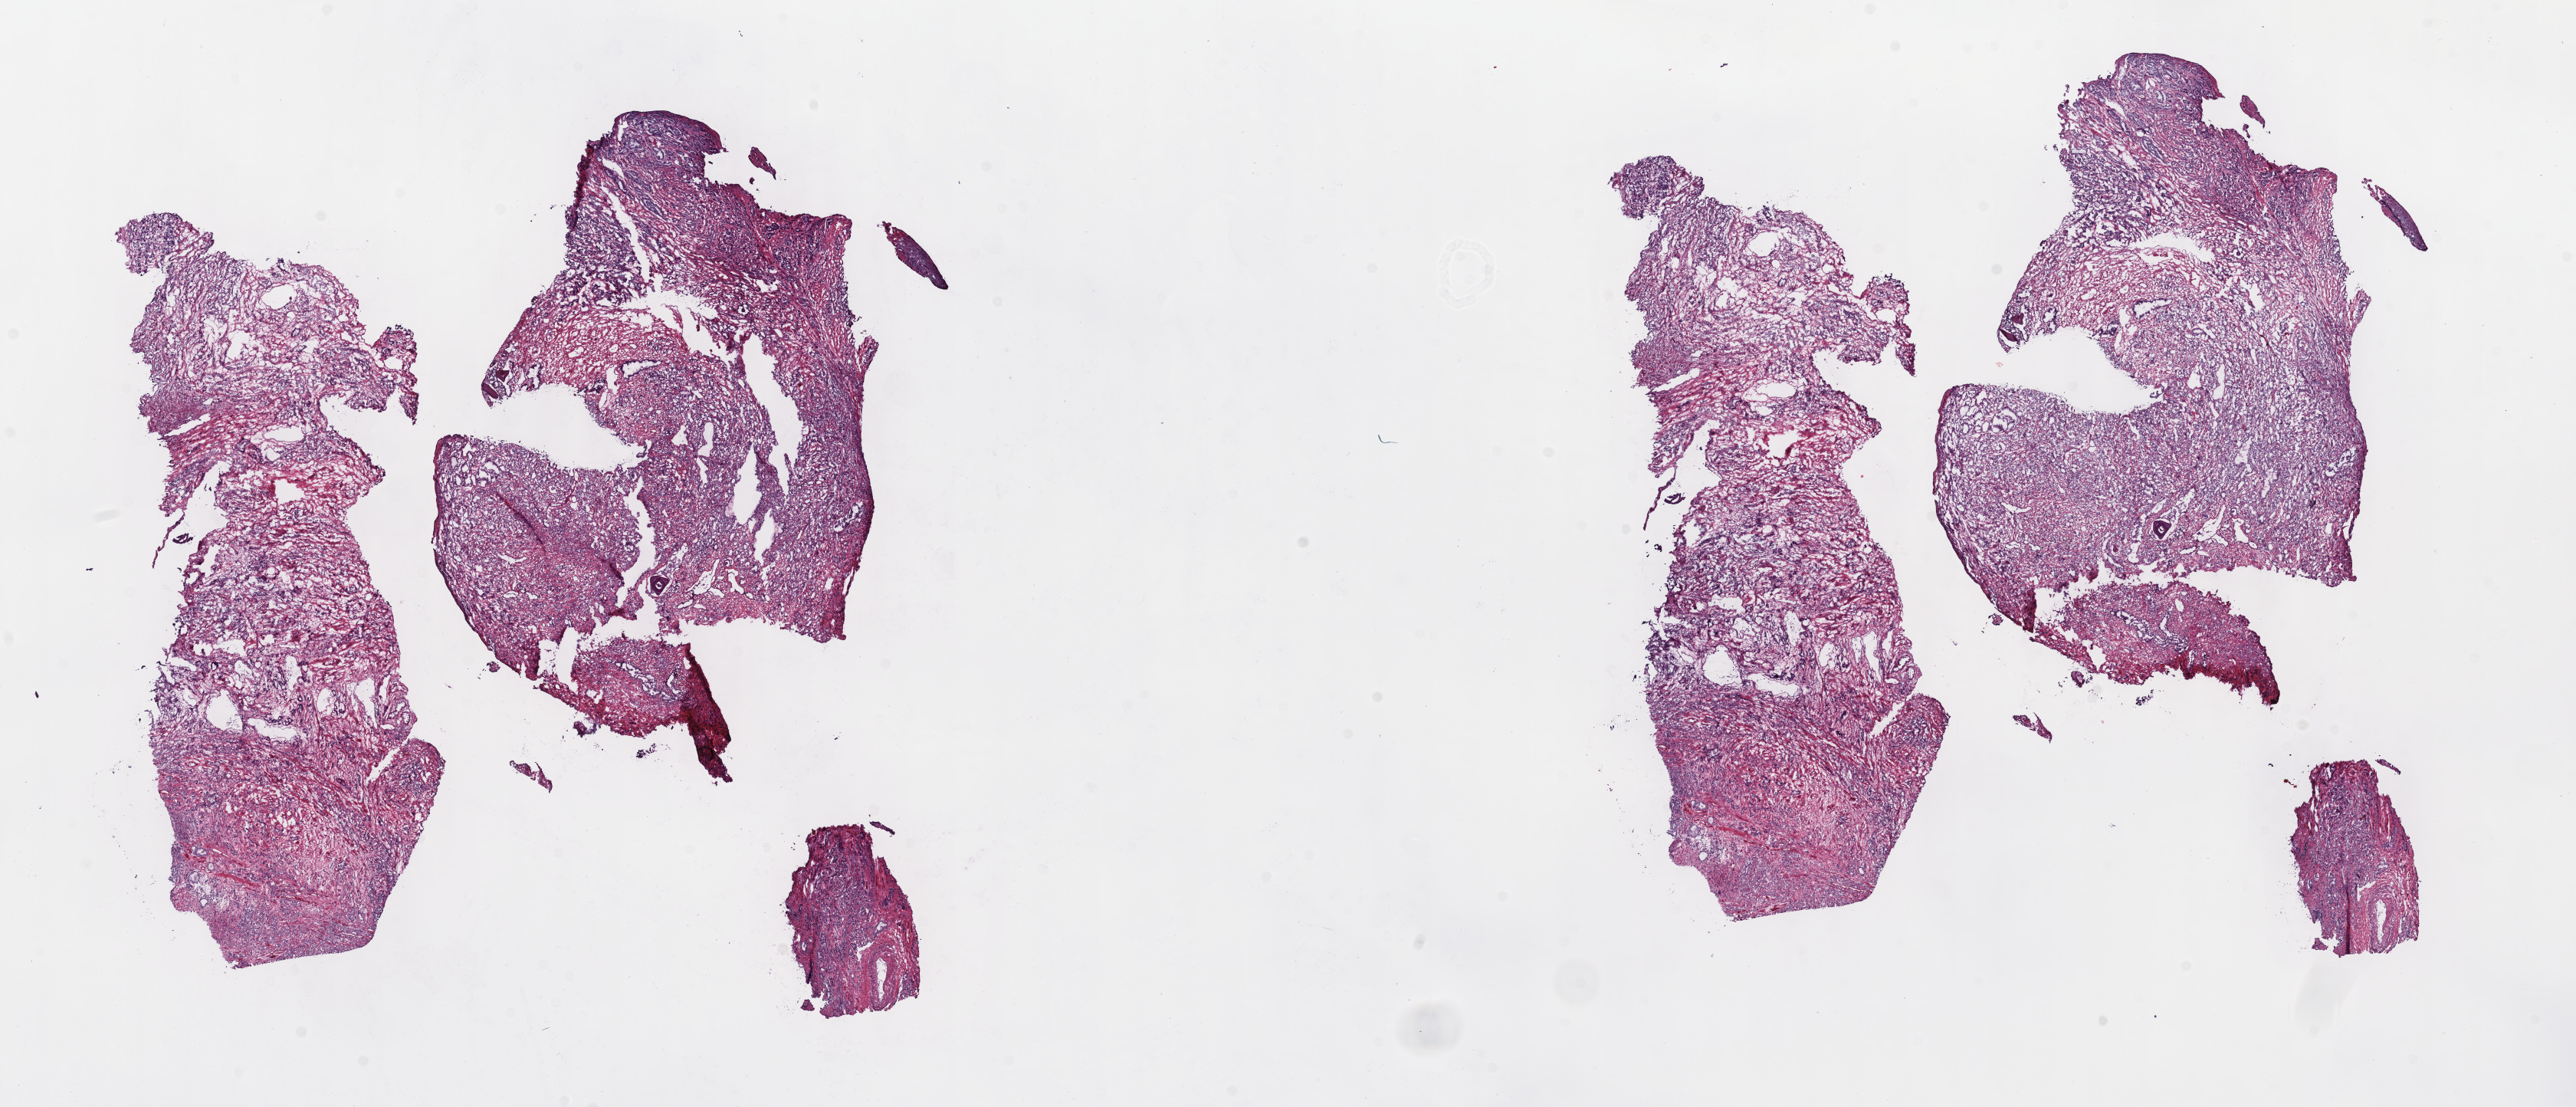
Whole-slide histology image, H&E, shown as a low-resolution overview of the whole scanned area (about 27.2 x 11.7 mm, from a 40x scan), frozen section, prostate, primary tumour sample. Patient: male, age at initial diagnosis 55 years. Gleason score: 7 (4+3). Composition of this section per pathologist review: tumour cells 70%, tumour nuclei 80%, normal cells 10%, stromal cells 20%, necrosis 0%. Infiltration values recorded for this section: lymphocyte infiltration 0%, monocyte infiltration 0%, neutrophil infiltration 0%.
Histologic diagnosis: Adenocarcinoma, NOS. Laterality: bilateral.